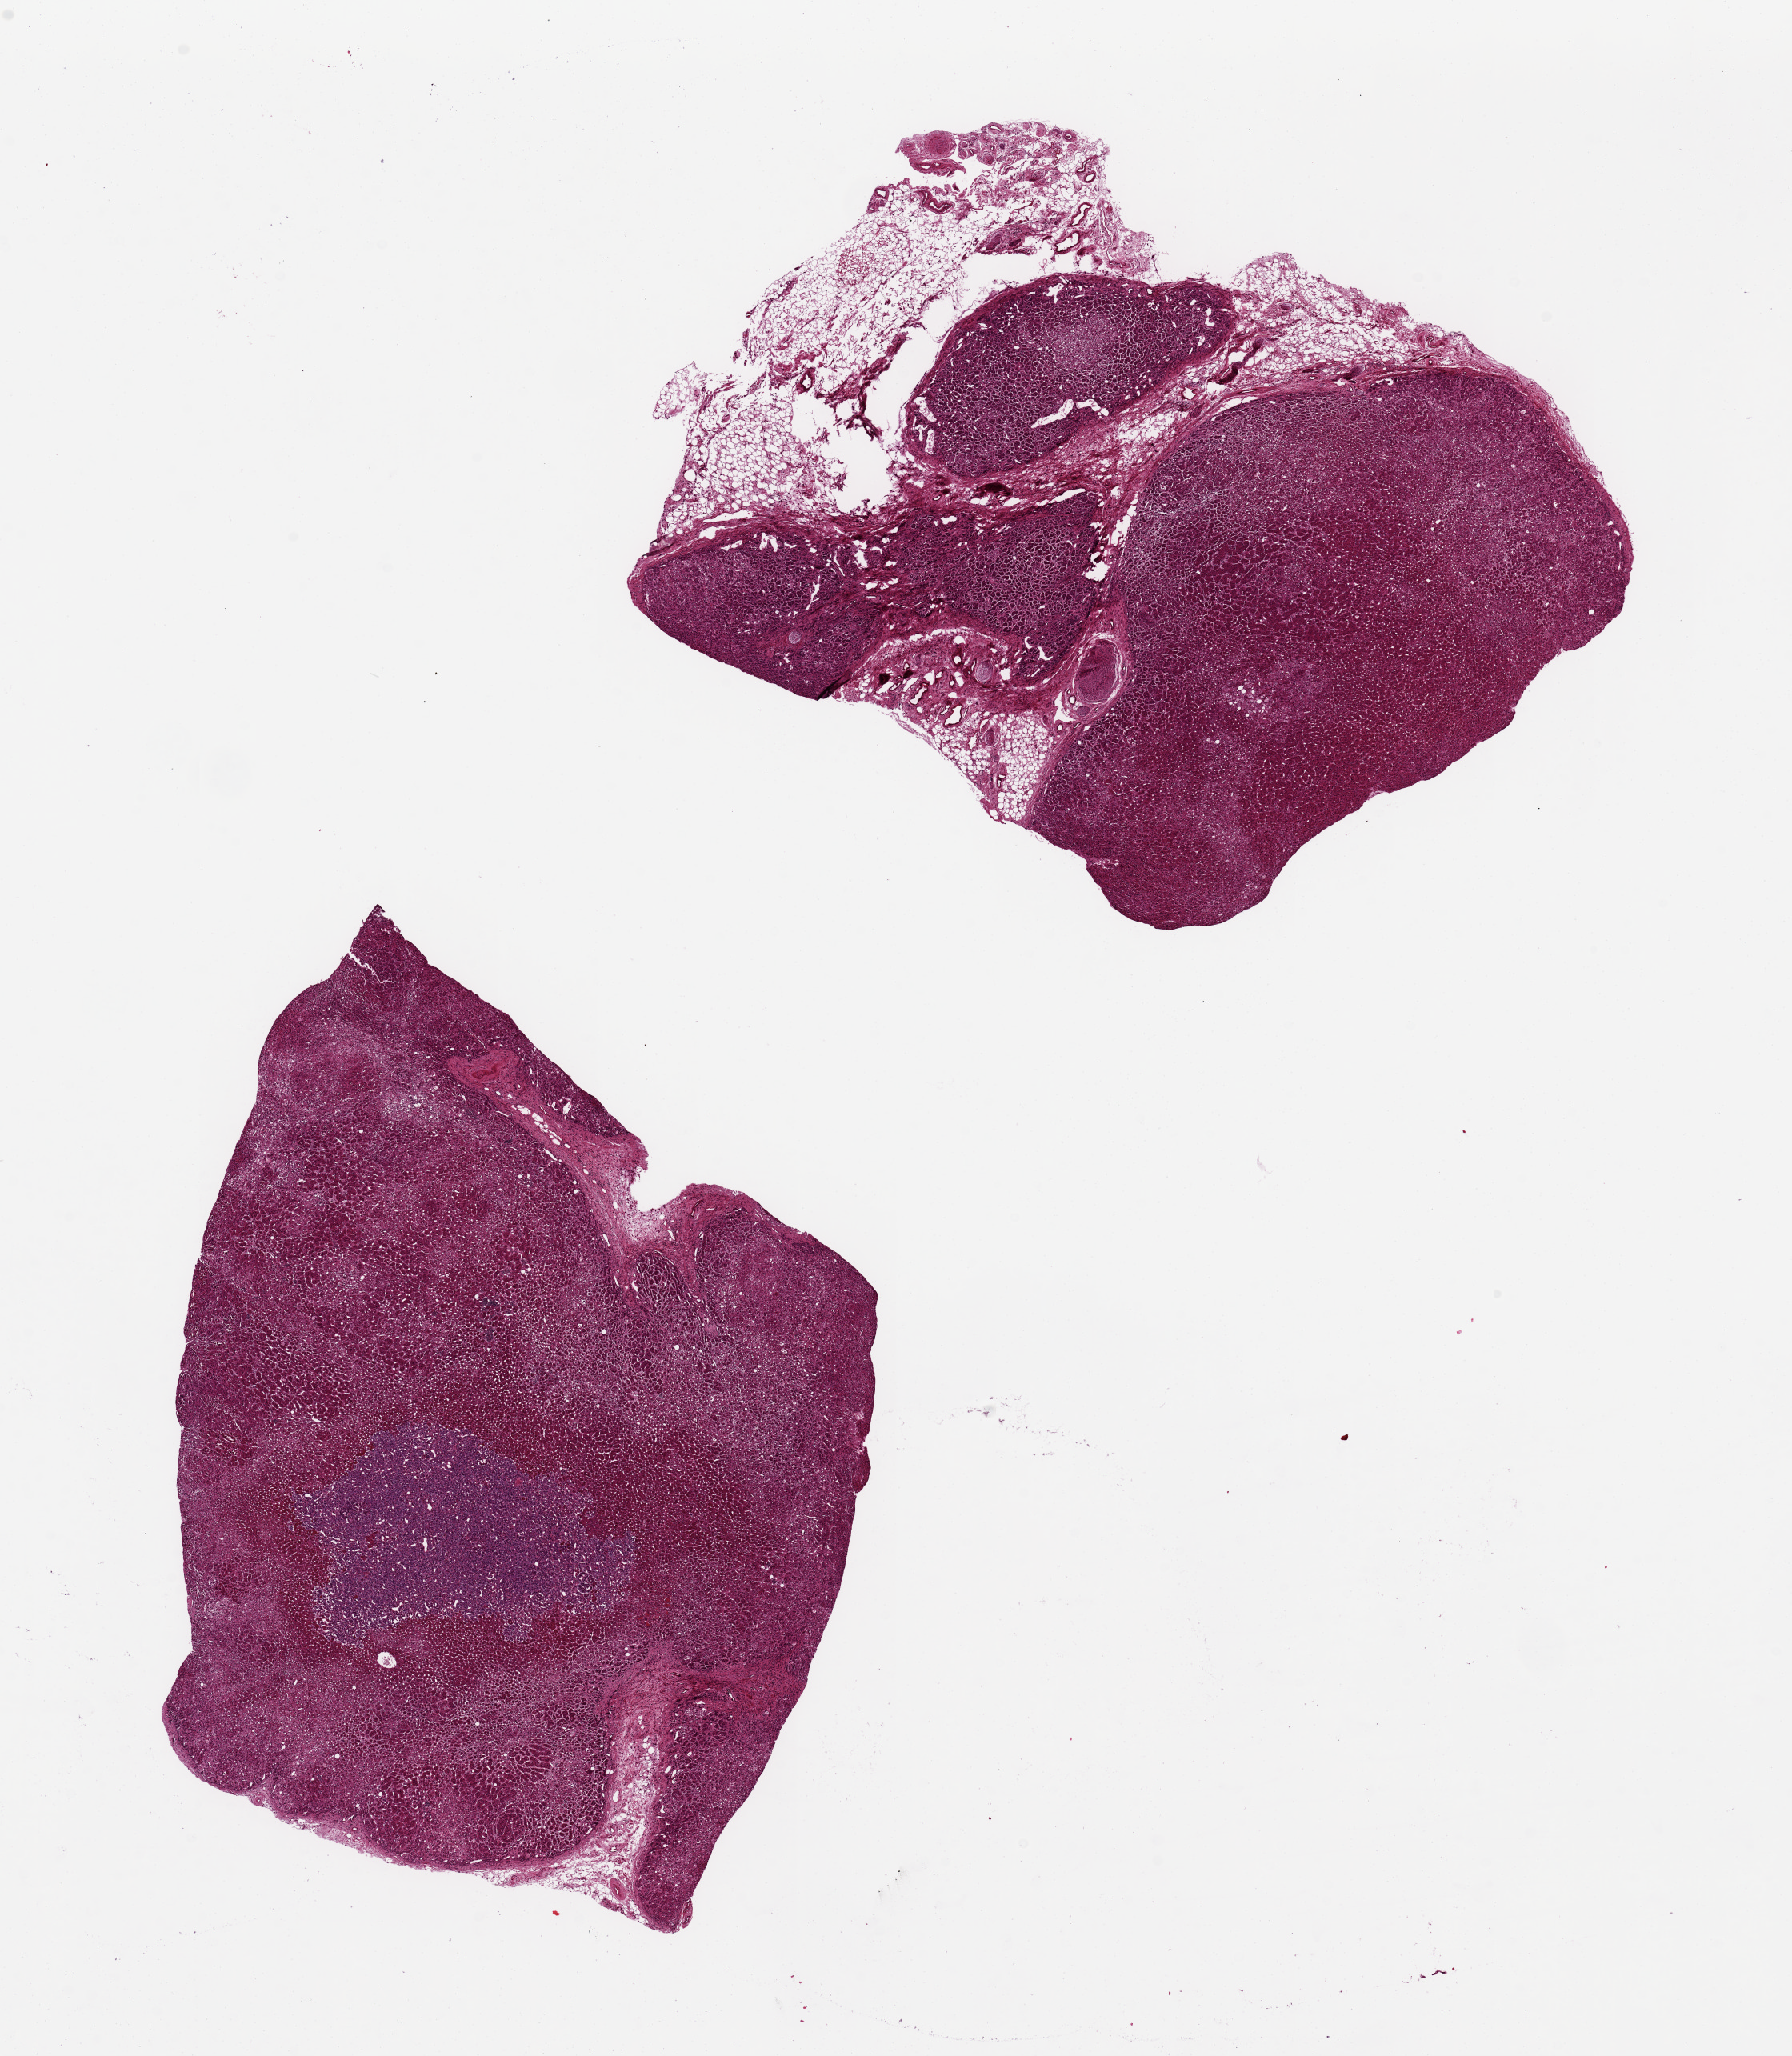
Haematoxylin and eosin whole-slide image, brightfield — a low-resolution overview of the entire scanned area, about 17.7 x 20.3 mm. PAXgene-fixed paraffin-embedded (PFPE) section. Section of adrenal gland (target tissue). Donor tissue sample. Donor sex: male.
Review note (as recorded): 2 pieces 8x6 & 7x7 mm; cortex; one has ~30% adipose.